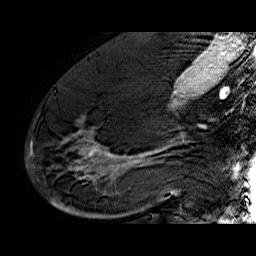
Breast MRI (dynamic contrast-enhanced), one sagittal slice; position 33 of 60 along the scan axis; dynamic contrast-enhanced series, time point 2 of 6 at this slice position (early post-contrast); 1.5 T; TE 6.4 ms, TR 32.9 ms; 4 mm slice thickness; 256 × 256 image matrix. Female patient. Case-level facts recorded for this patient, not image findings: setting: breast cancer imaged before/during neoadjuvant chemotherapy; receptor status: HR-positive, HER2-negative.
Structures marked on this image (semi-automatic segmentation, software-assisted and operator-edited):
- analysis volume of interest (the breast-tissue region the enhancement analysis was run in; not a lesion): bounding box <40,74,176,210> (left, top, right, bottom; pixels)
- tumour enhancement mask (voxels above the 100 % enhancement threshold inside the analysis volume of interest): <66,130,176,195>